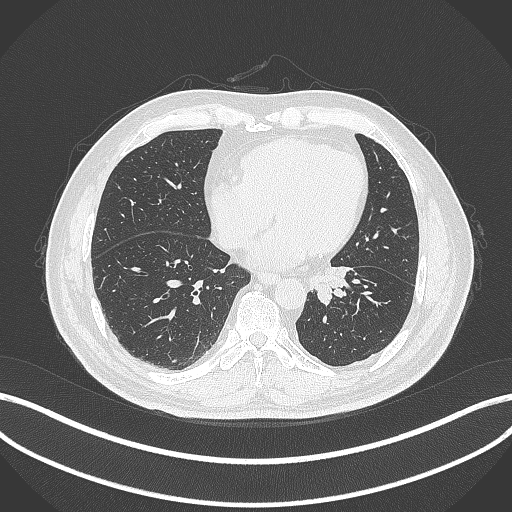
Chest CT, one axial slice. Position 92 of 312 along the scan axis. Reconstruction kernel B70f. Lung window (W 1500 / L -600 HU). 1 mm slice thickness. 512 × 512 image matrix. Patient: male, 71 years. Case-level facts recorded for this patient, not image findings: clinical TNM (as recorded): T1b N0 M0.
Structures marked on this image (rectangle marked by the reading radiologist):
- lung tumour (recorded histology: squamous cell carcinoma): bounding box <309,264,353,308> (left, top, right, bottom; pixels)